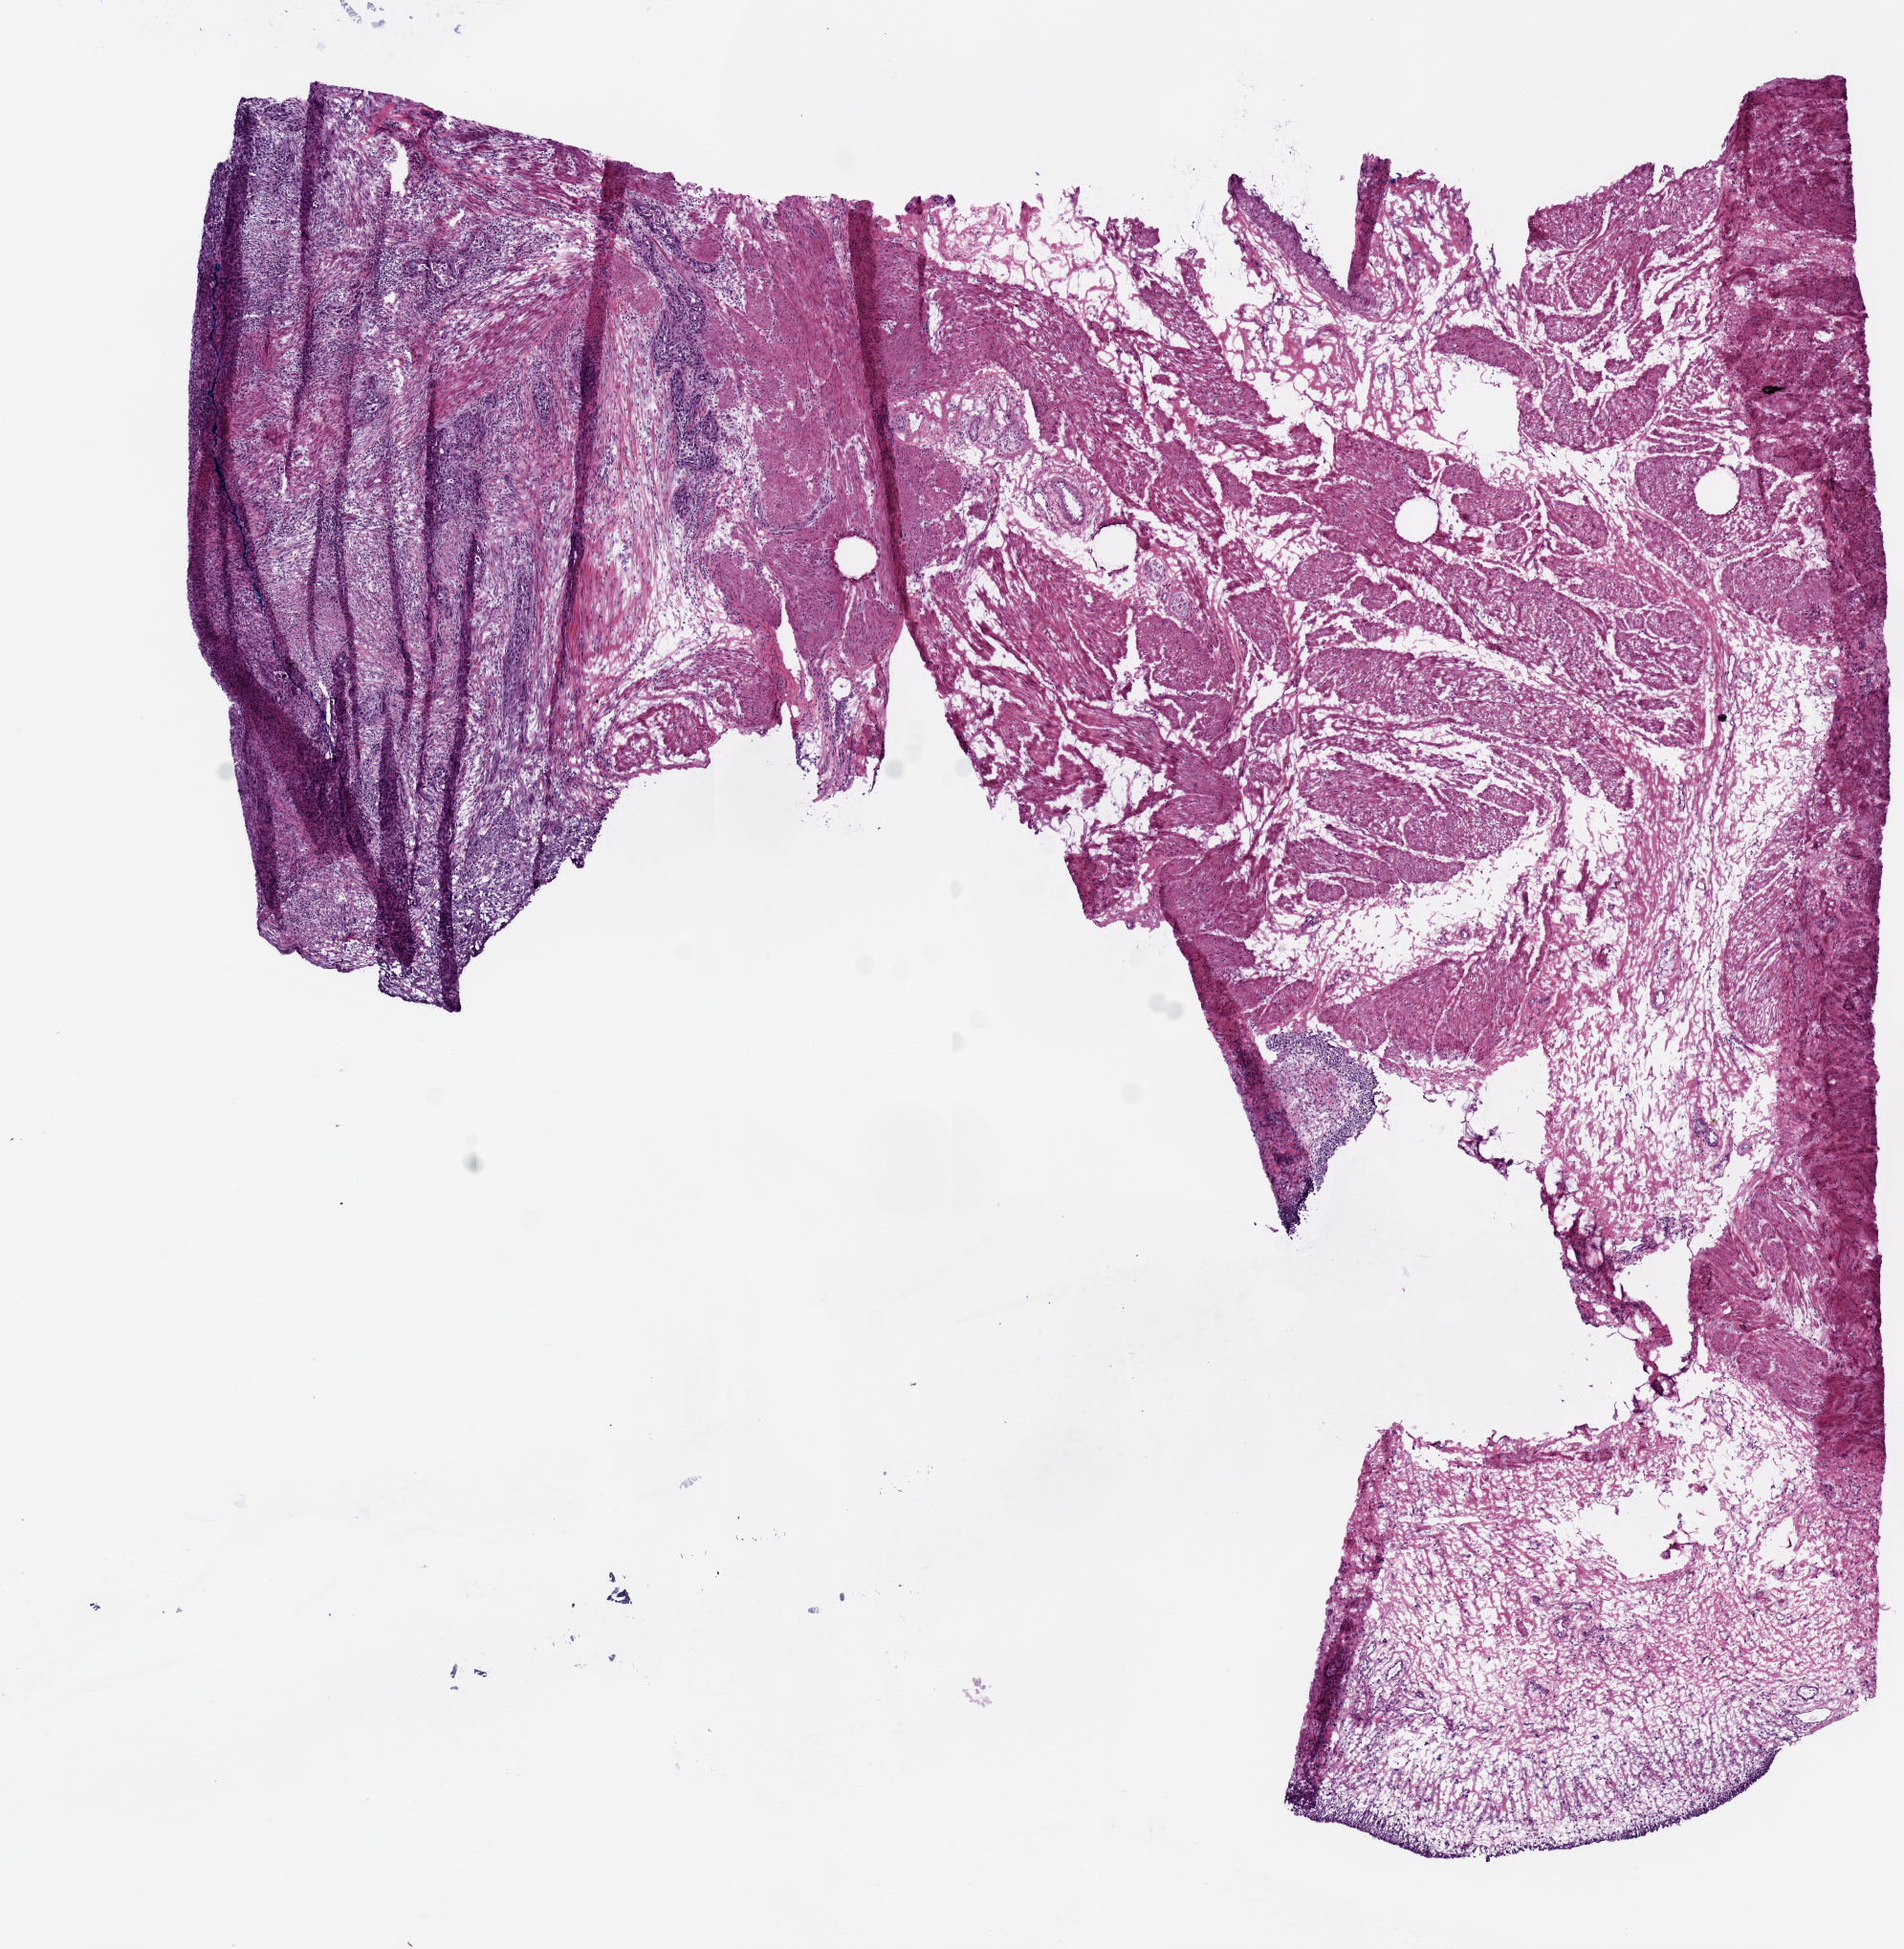
Digitized H&E-stained tissue section (whole slide), a low-resolution overview of the entire scanned area, about 7.9 x 8.1 mm (acquisition: 20x scan). Frozen section from the top of the tissue portion. Bladder, primary tumour sample. Male, age 79 years at initial diagnosis. Histologic grade: high grade. Slide review estimates, as recorded: tumour cells 80%, tumour nuclei 60%, normal cells 0%, stromal cells 20%, necrosis 0%. Inflammatory infiltration, as recorded: lymphocyte infiltration 0%, monocyte infiltration 0%, neutrophil infiltration 0%.
TNM: T2b N0 M0. Diagnosis: Transitional cell carcinoma. AJCC pathologic stage: II (7th edition).